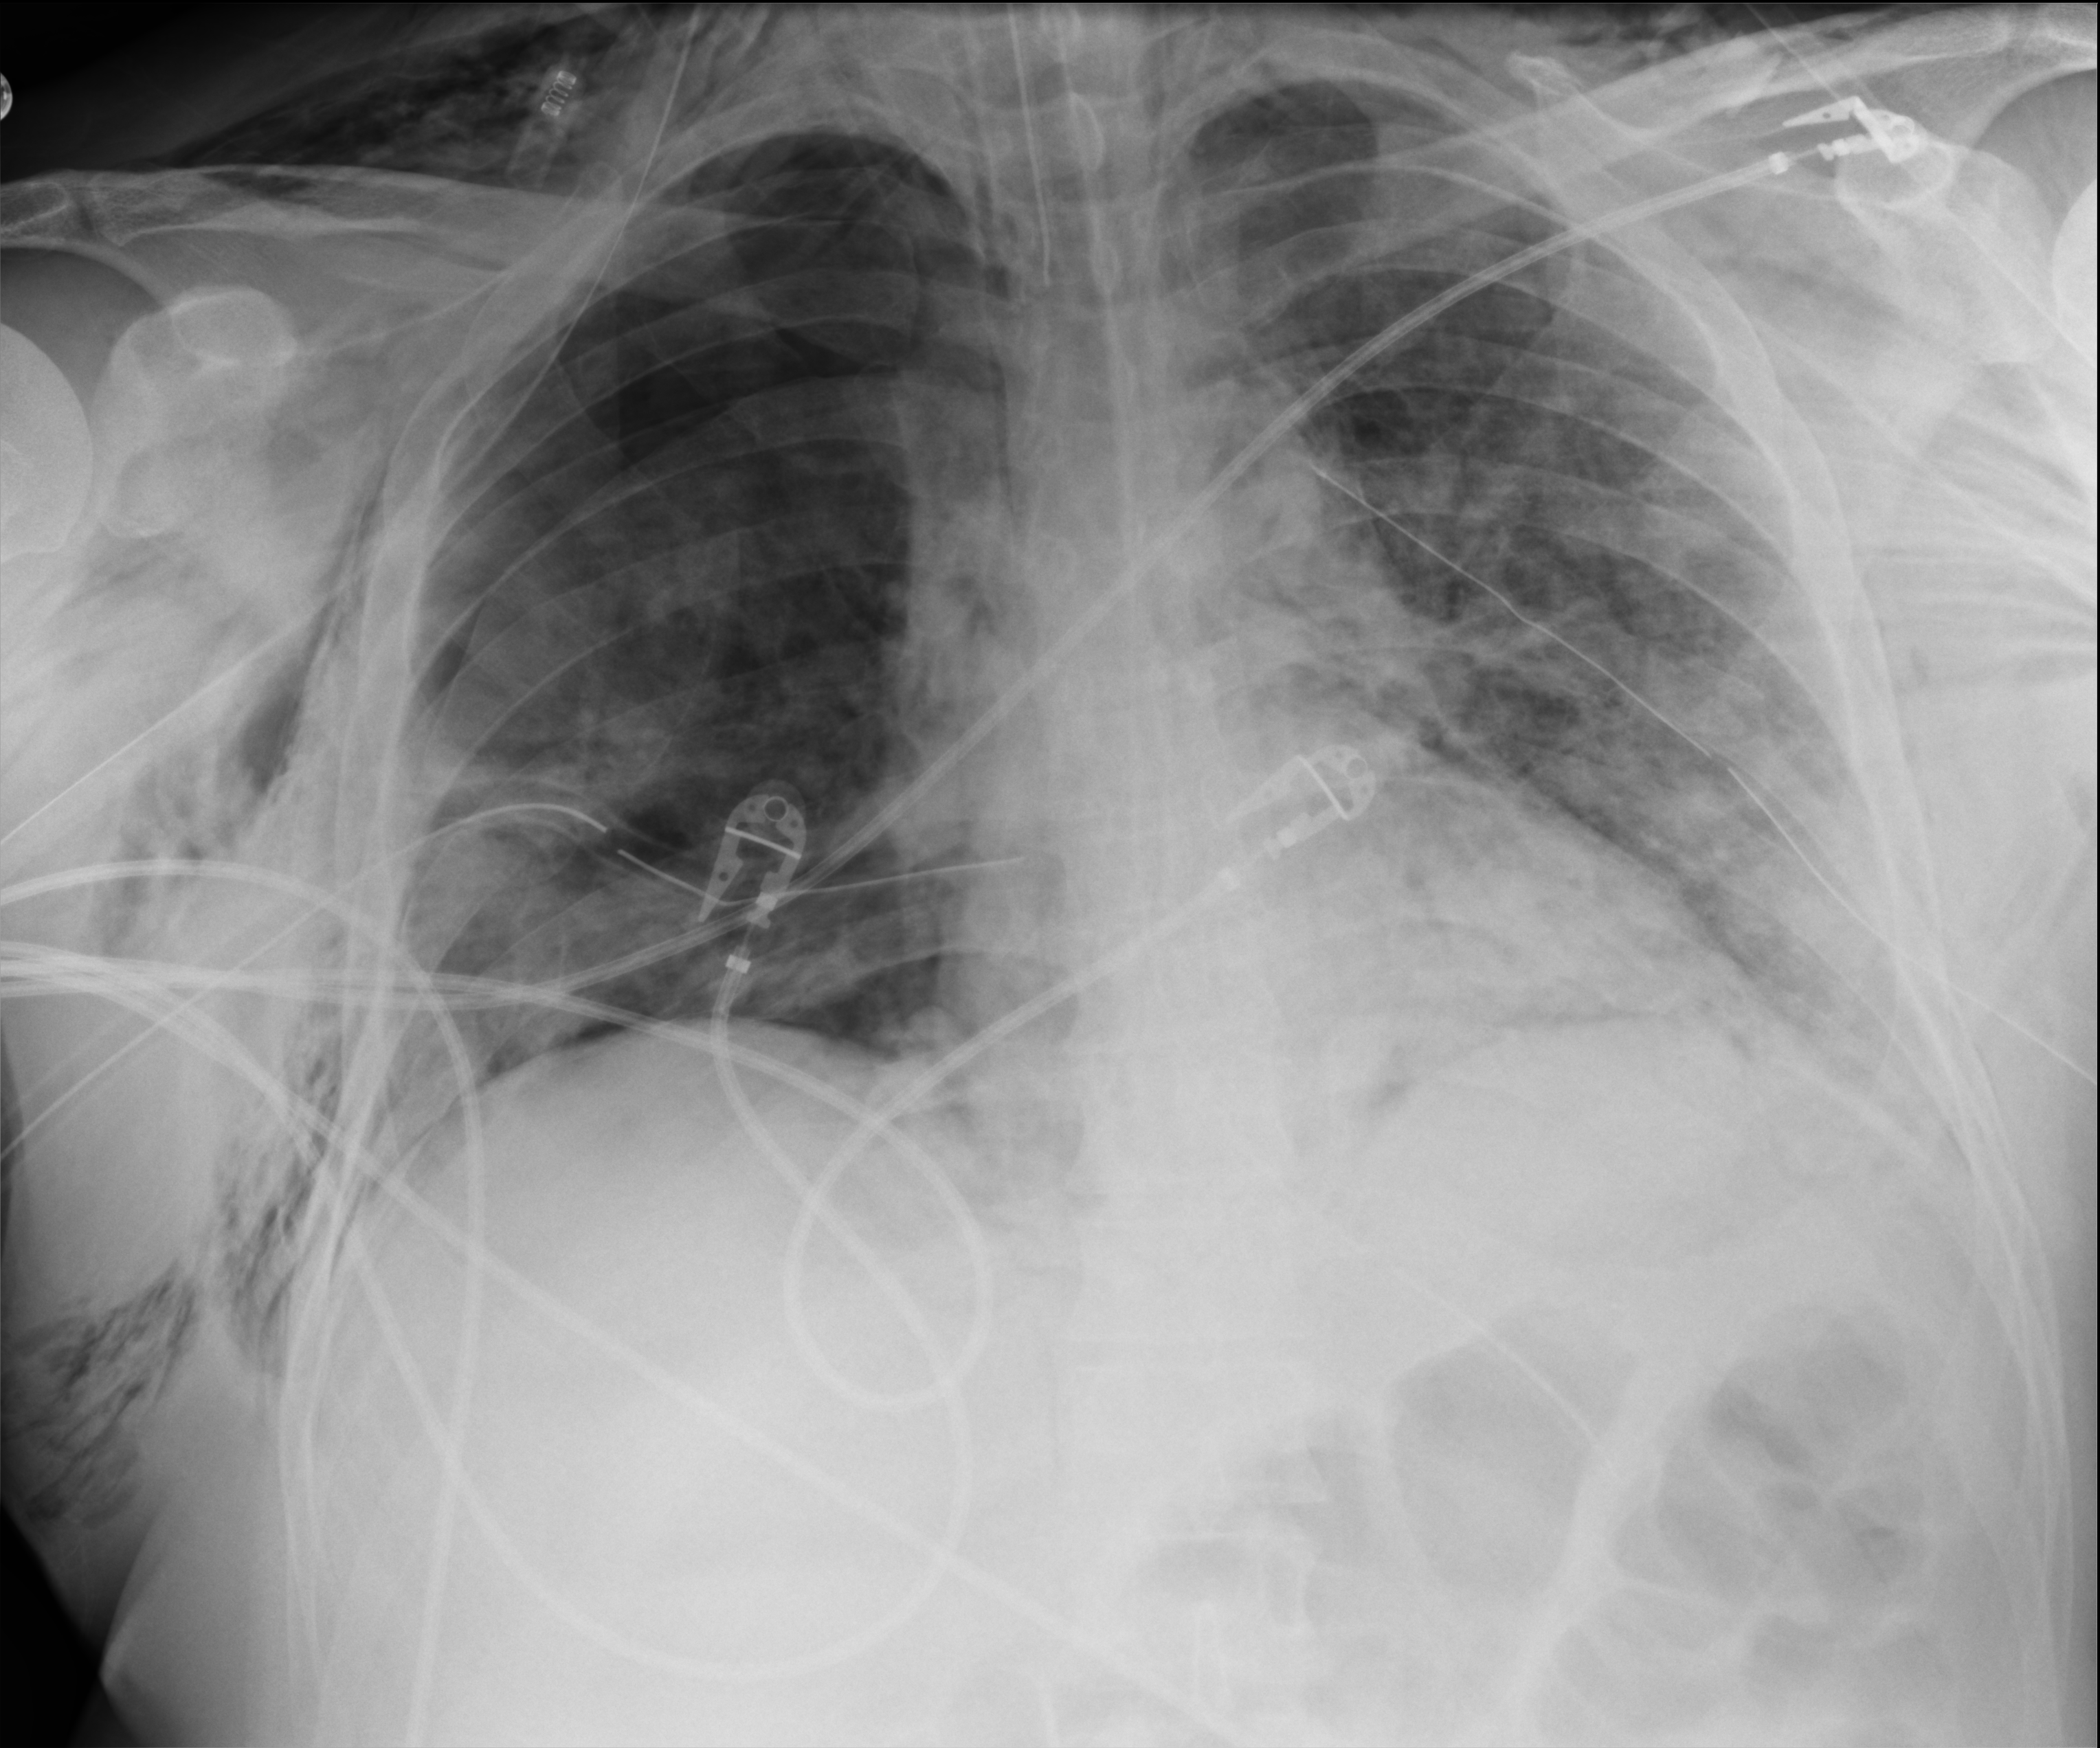
Bedside chest radiograph (computed radiography), anteroposterior (AP) projection. Male patient hospitalised with COVID-19, age 18–59 years.
From the hospital-stay record, not from the radiograph (when in the stay this image was taken is not recorded):
- admitted to intensive care during this hospital stay: yes
- mechanically ventilated during this hospital stay: yes